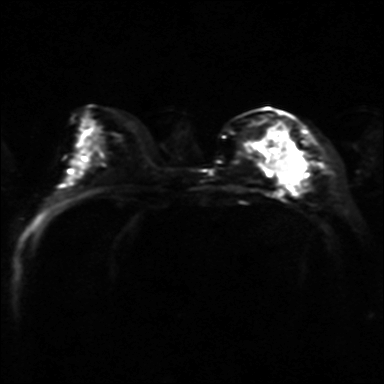
Breast MRI, one axial slice. Slice 14 of 36 in the series (ordered by position). Diffusion-weighted series; image 2 of 4 stored at this slice position (different b-values; order by instance number). 3 T. 4 mm slice thickness. 384 × 384 image matrix, field of view 320 × 320 mm. Female patient.
Structures marked on this image (outlined manually by an expert reader):
- tumour on diffusion-weighted imaging: bounding box [x1, y1, x2, y2] px = [275, 152, 302, 184]